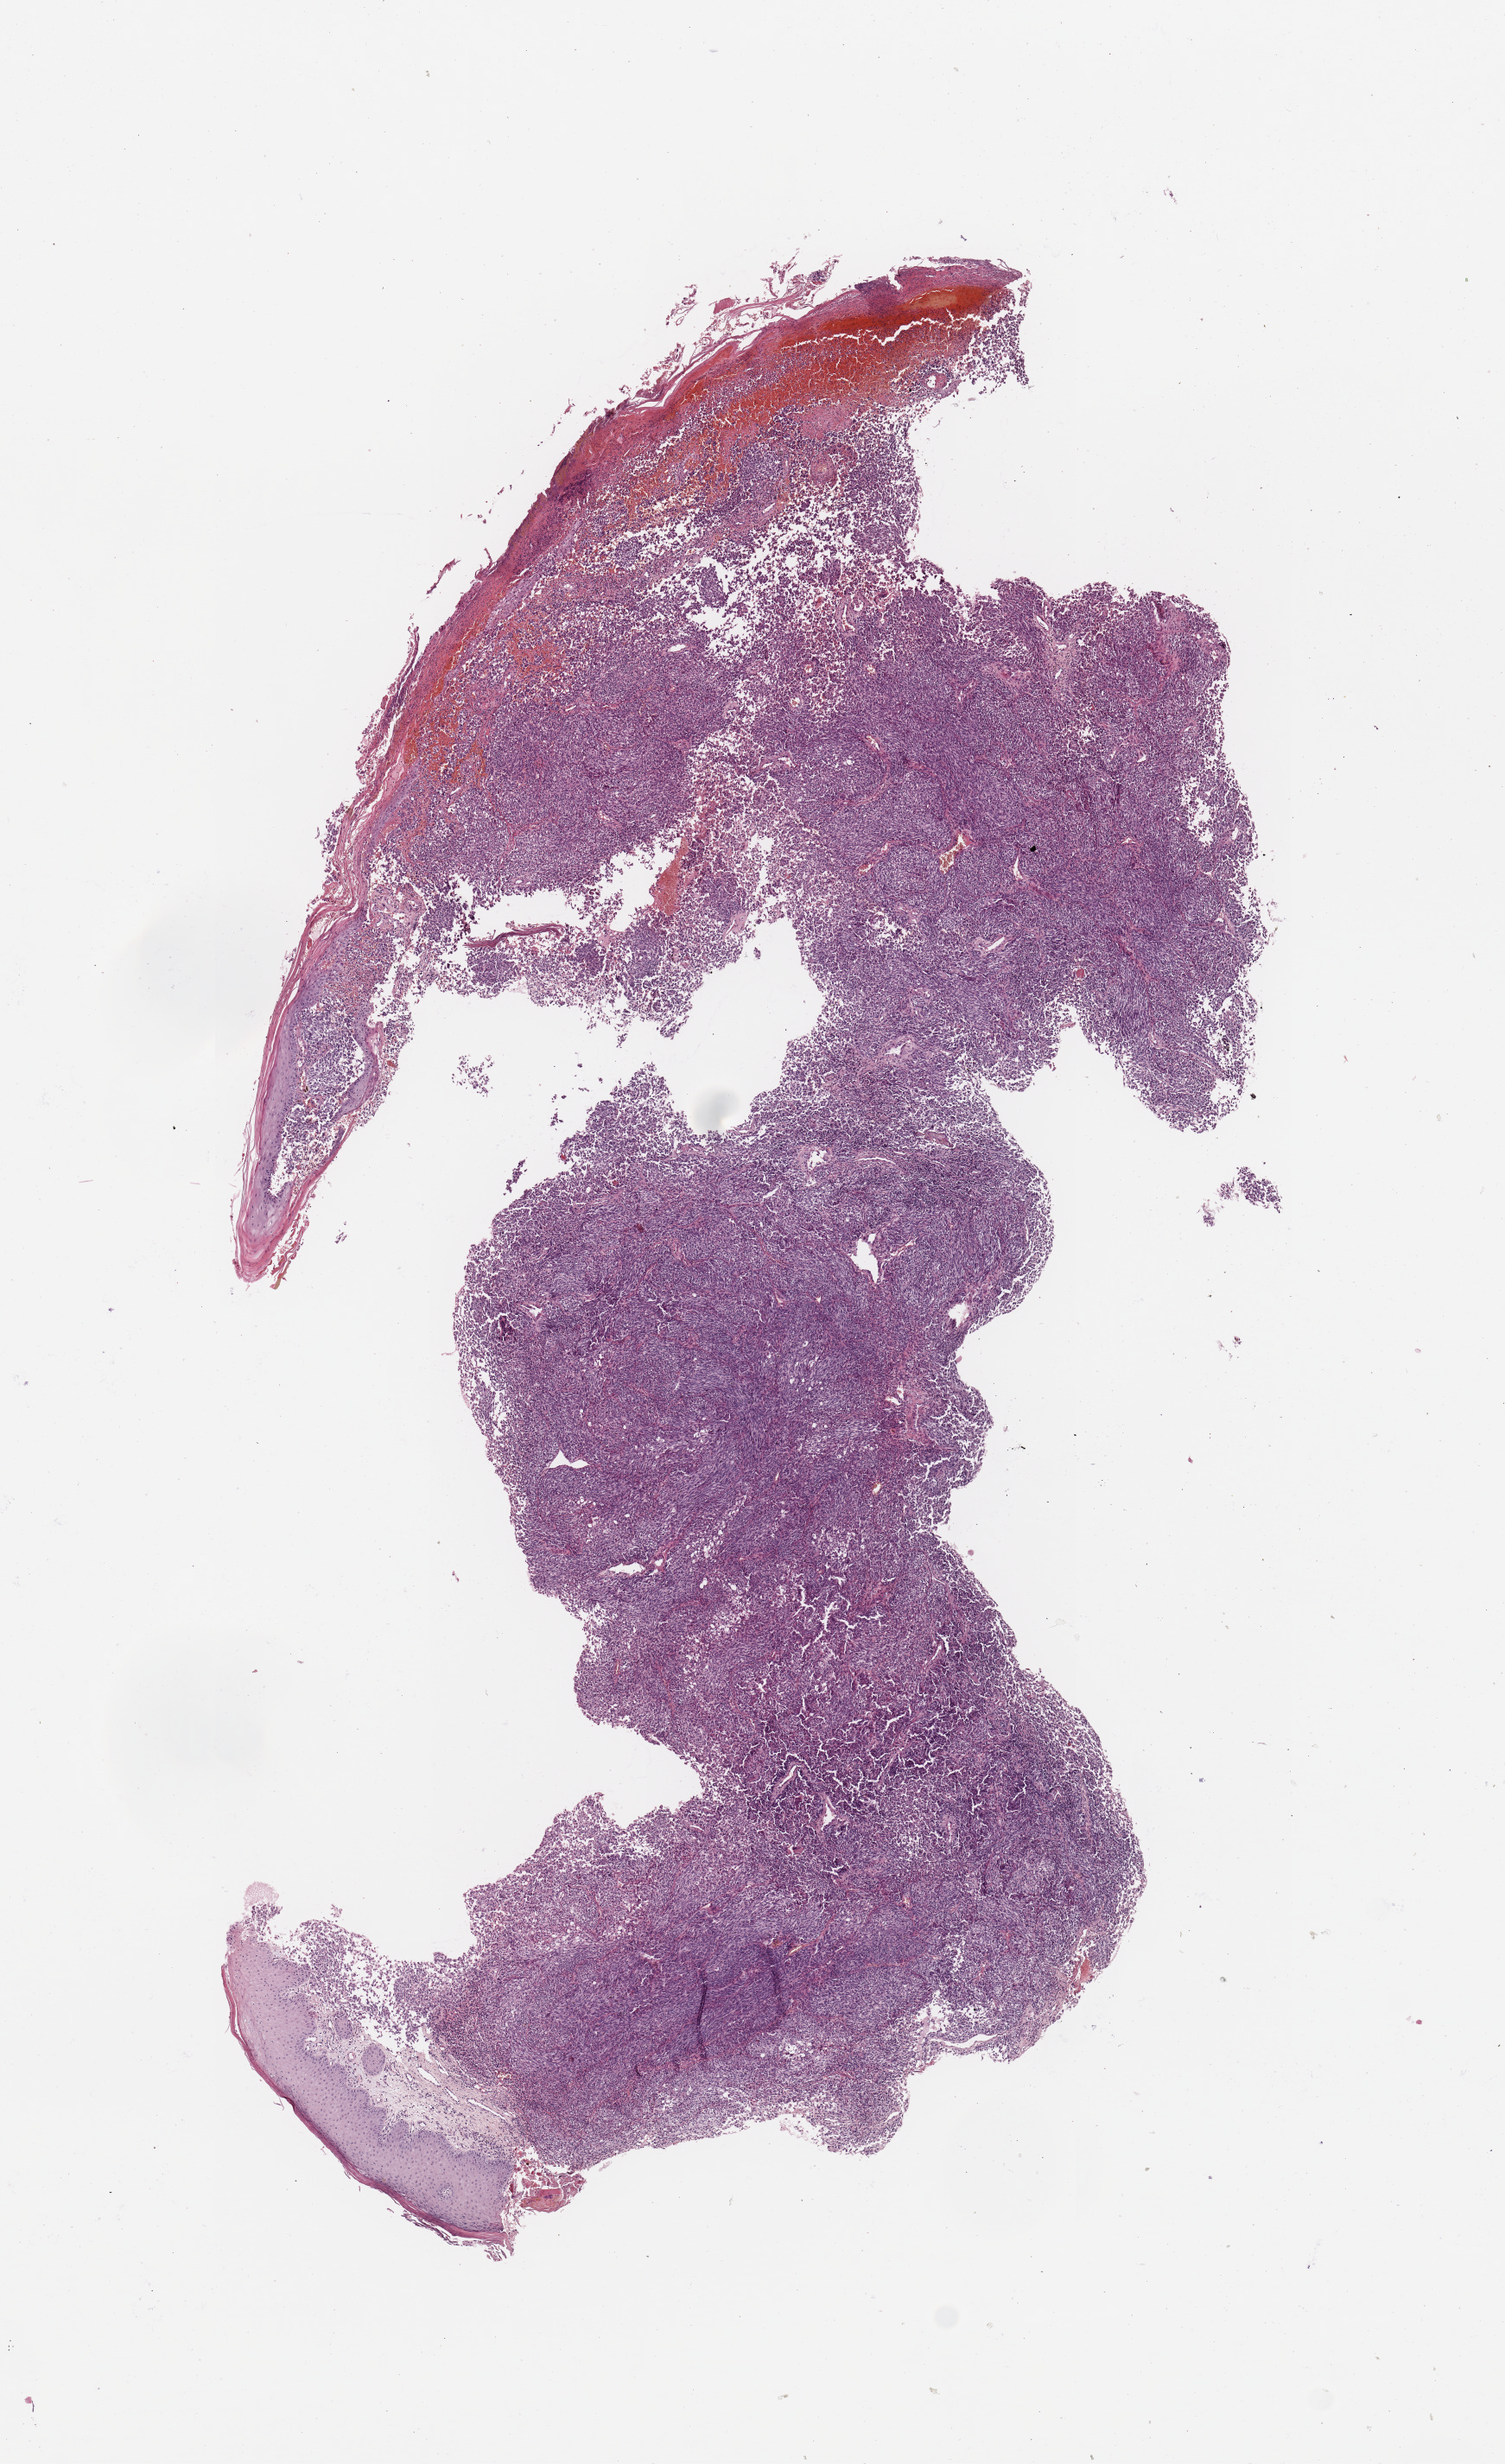
Digitized H&E-stained tissue section (whole slide), shown as a low-resolution overview of the whole scanned area (about 6.9 x 11.3 mm, acquisition: 20x scan). Melanoma tumour tissue; sampled site not recorded. 73-year-old male patient.
Histologic diagnosis: Malignant melanoma, NOS.